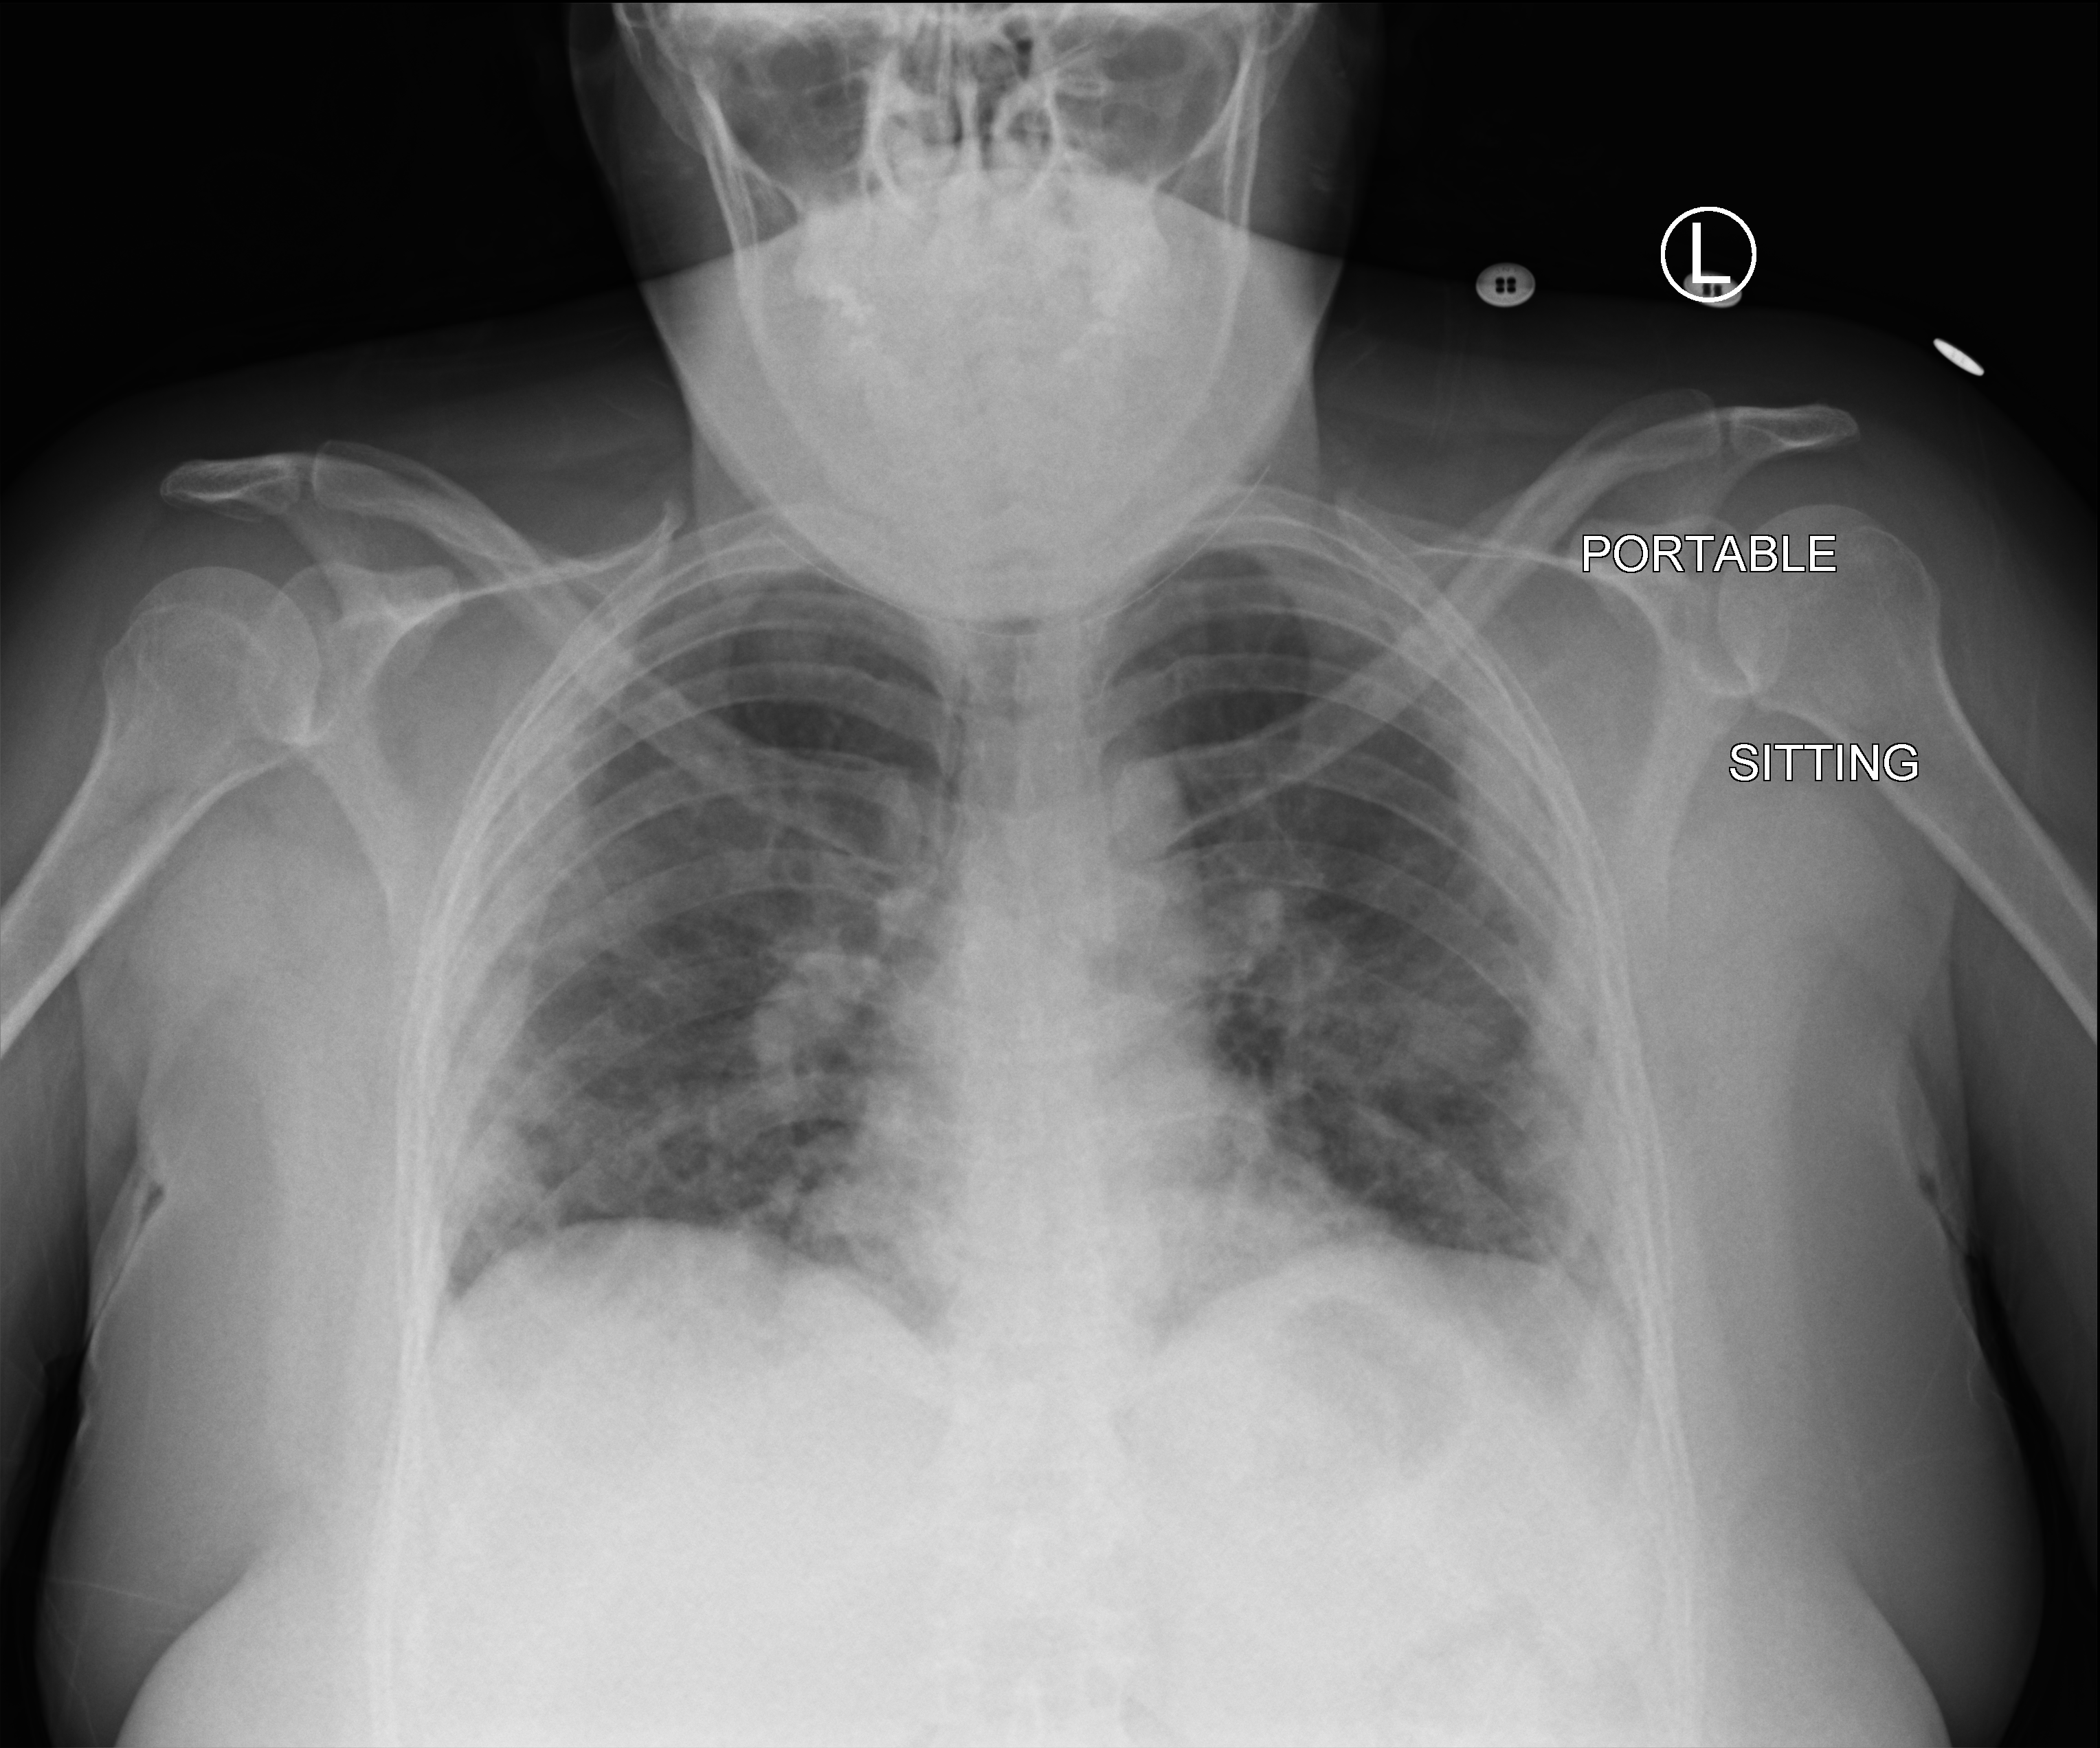
Portable chest radiograph; anteroposterior (AP) projection. Female patient hospitalised with COVID-19, age 18–59 years.
Hospital-stay facts (about this admission, not read from this image; timing relative to this image not recorded): other chronic lung disease (admission record): no.